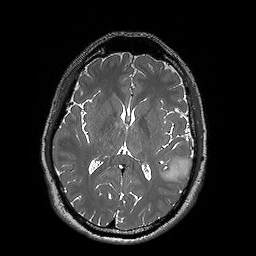
Brain MRI from a brain-tumour surgery series, one axial slice; slice 85 of 192 in the series (ordered by position); 256 × 256 image matrix, field of view 250 × 250 mm. From the clinical record (not read from this slice): histopathology: Oligodendroglioma; WHO grade: 2.
Outlined on this slice (manually delineated by an expert):
- tumour: bounding box (x1, y1, x2, y2) in pixels: (159, 156, 193, 180)